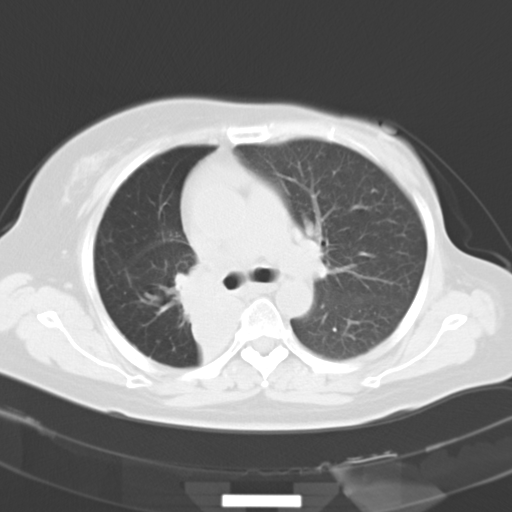
Chest CT, one axial slice. Position 20 of 30 along the scan axis. Reconstruction kernel B40f. 120 kVp. Lung window (W 1500 / L -600 HU). 8 mm slice thickness. 512 × 512 image matrix, field of view 331 × 331 mm. Female patient, age 53 years. From the clinical record (not read from this slice): clinical TNM (as recorded): T2b N1 M0.
Outlined on this slice (rectangle marked by the reading radiologist):
- lung tumour (recorded histology: adenocarcinoma): box from (x=171, y=262) to (x=231, y=339) px